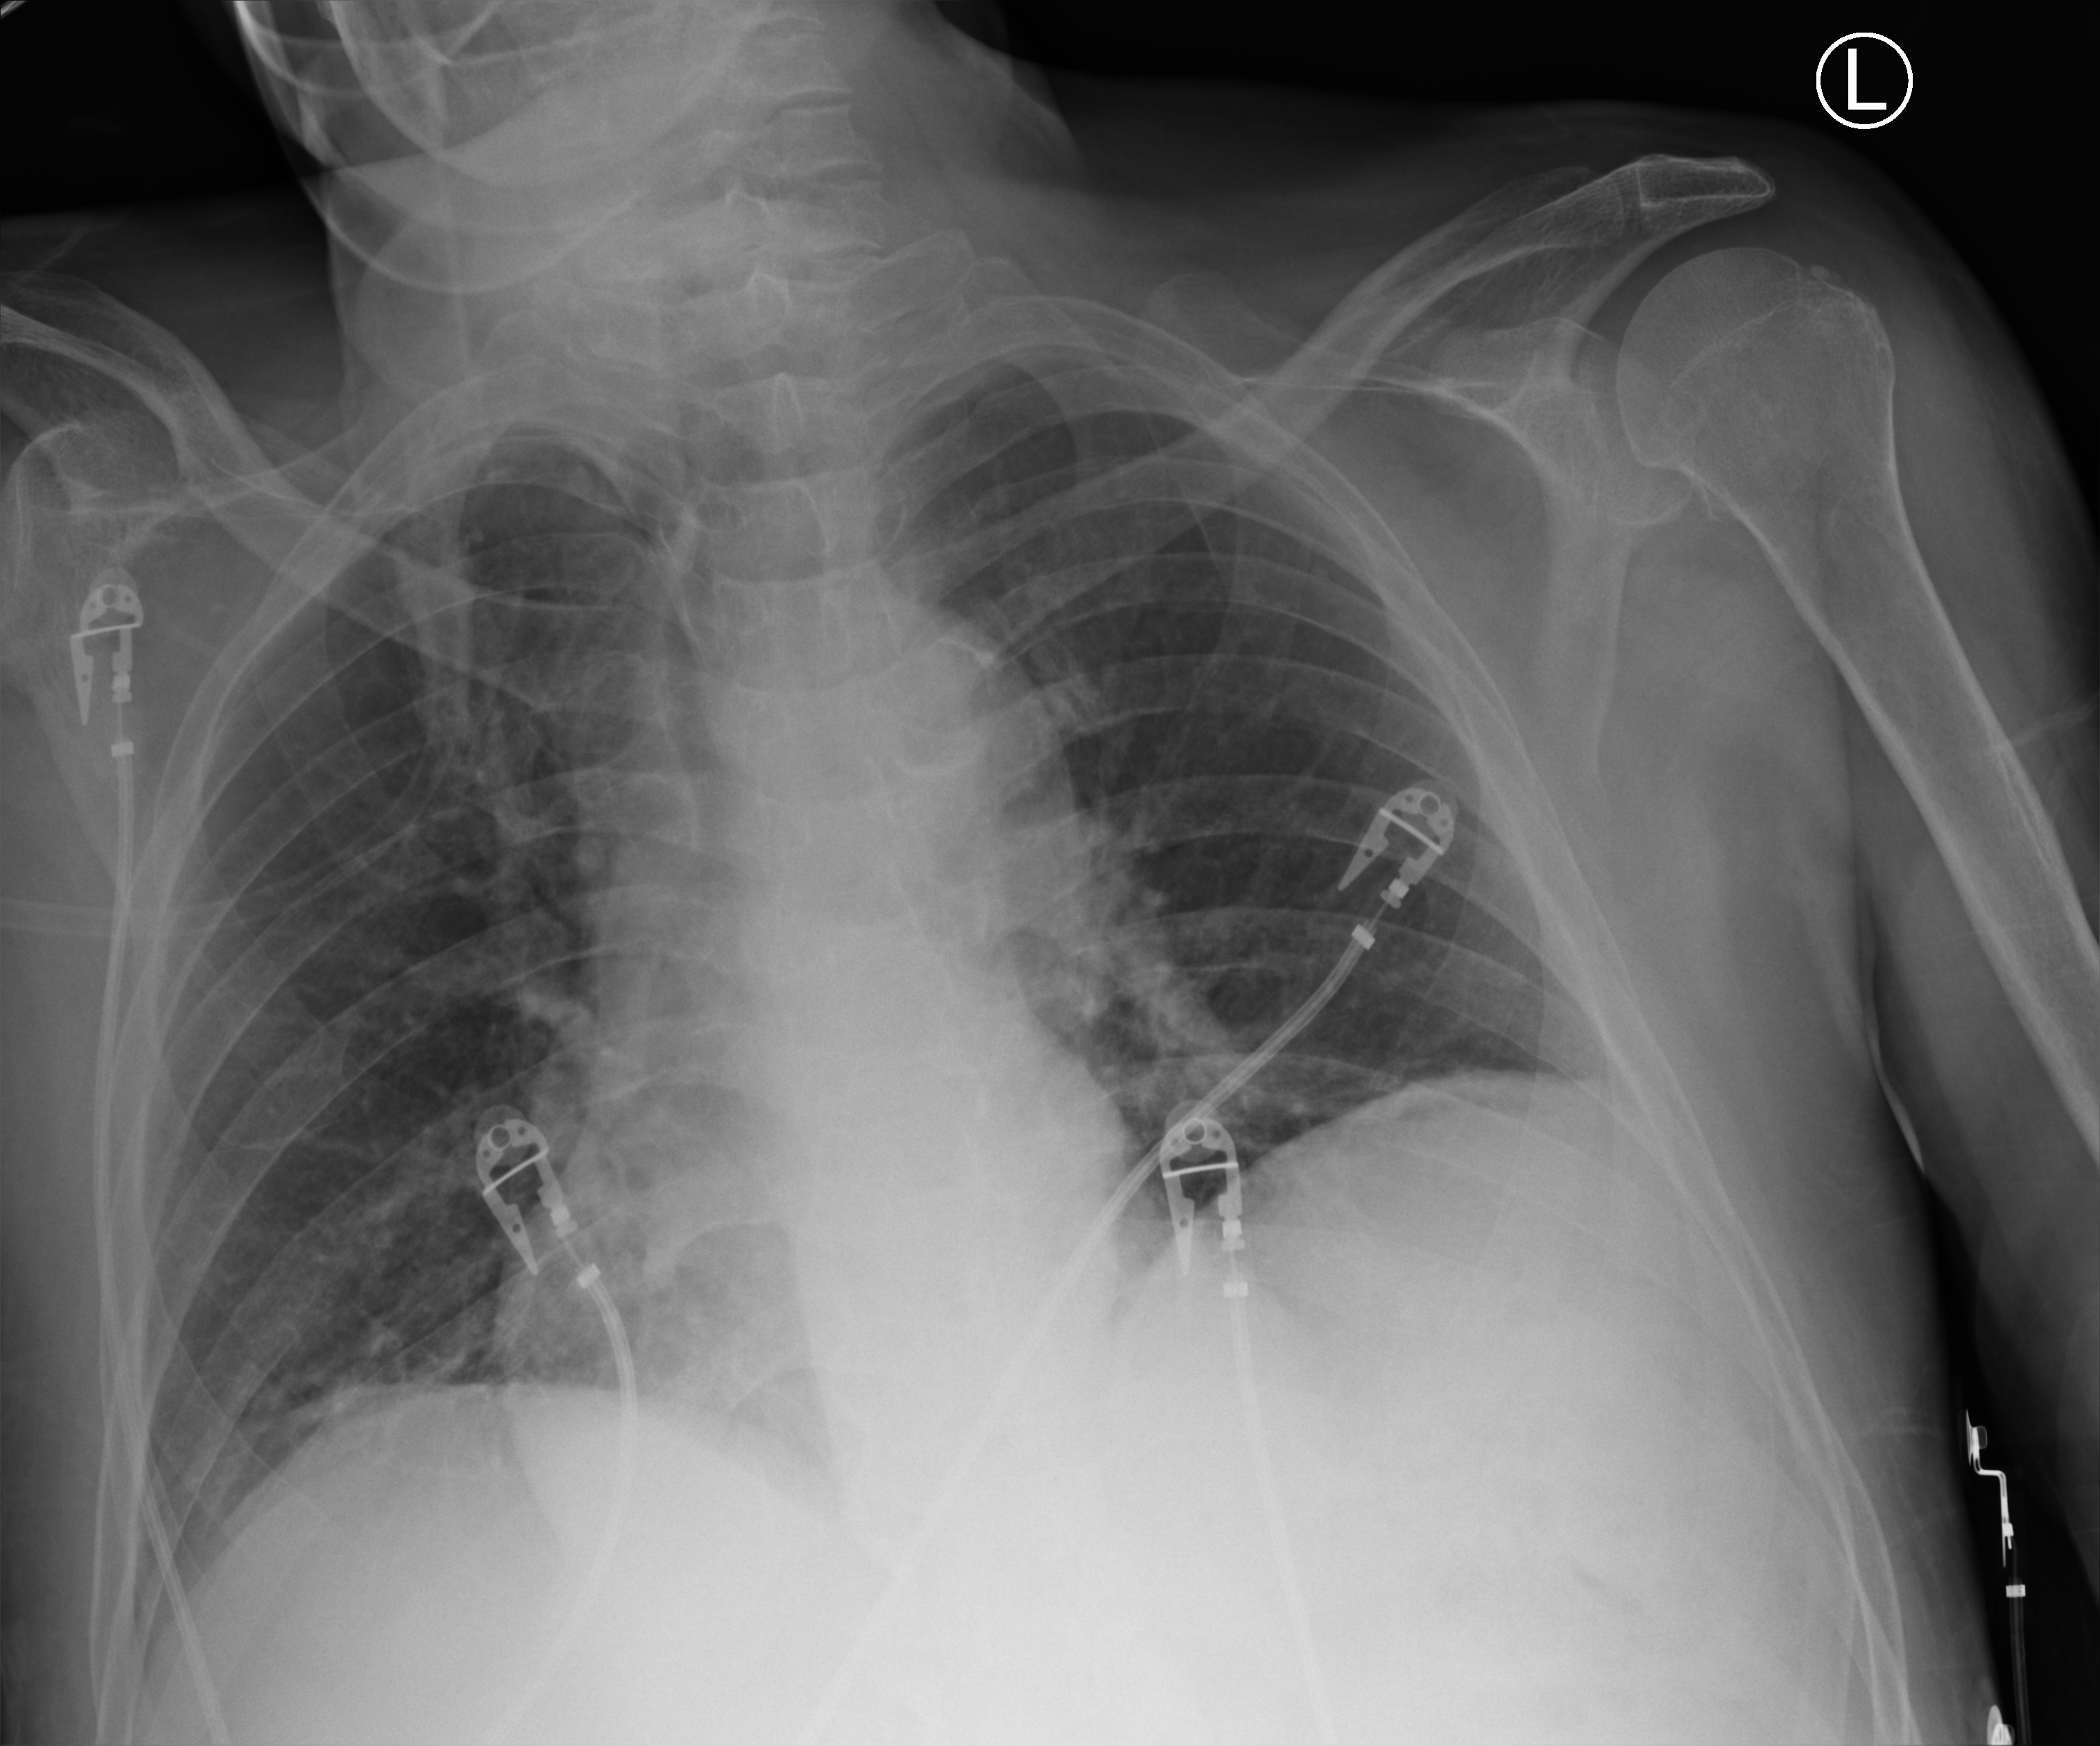
Bedside chest radiograph (computed radiography), anteroposterior (AP) projection. Patient hospitalised with COVID-19; male, aged 75–90 years.
From the hospital-stay record, not from the radiograph (when in the stay this image was taken is not recorded): mechanically ventilated during this hospital stay: no; admitted to intensive care during this hospital stay: no; smoking status (admission record): never.